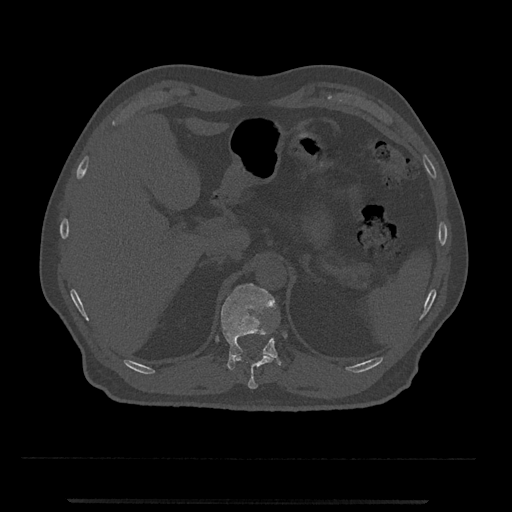
CT including the spine, one axial slice; slice 430 of 797 in the series (ordered by position); bone window (W 1800 / L 400 HU); 0.5 mm slice thickness; 512 × 512 image matrix, field of view 419 × 419 mm. Male patient, age 63 years. From the clinical record (not read from this slice): primary cancer: prostate.
Structures marked on this image (semi-automatically segmented with operator editing):
- T11 vertebra: bounding box [x1, y1, x2, y2] px = [233, 353, 274, 389]
- T12 vertebra: [221, 283, 281, 370]